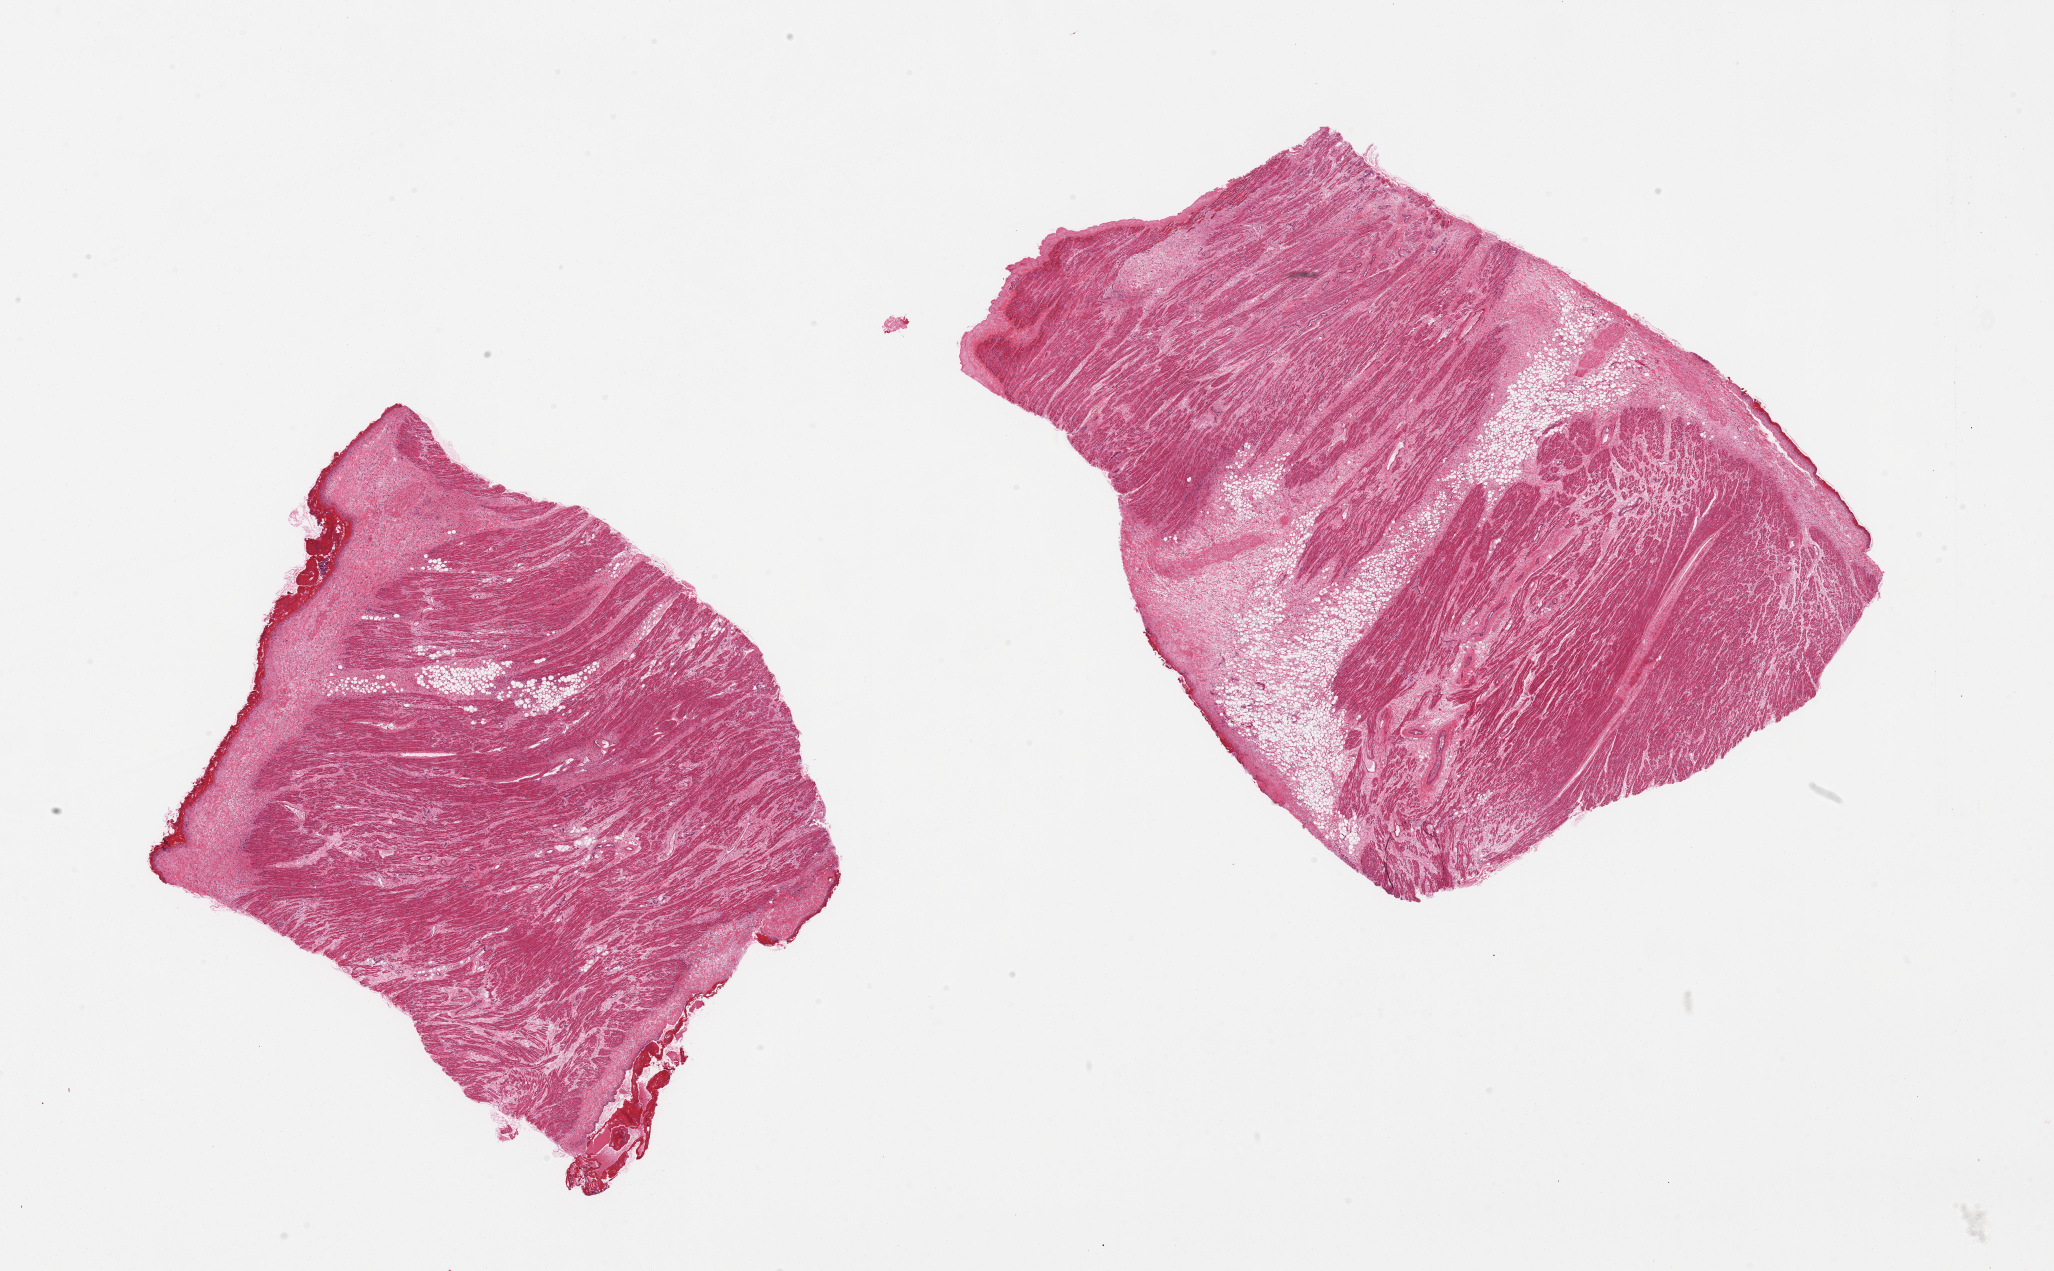
Digitized haematoxylin and eosin-stained section, whole scanned area (about 32.5 x 20.1 mm, acquisition: 20x scan) shown as a low-resolution overview; PAXgene-fixed paraffin-embedded (PFPE) section; section of auricular appendage (target tissue); tissue donor sample.
Reviewer comment on this tissue sample: 2 pieces, fat necrosis, fibrosis.